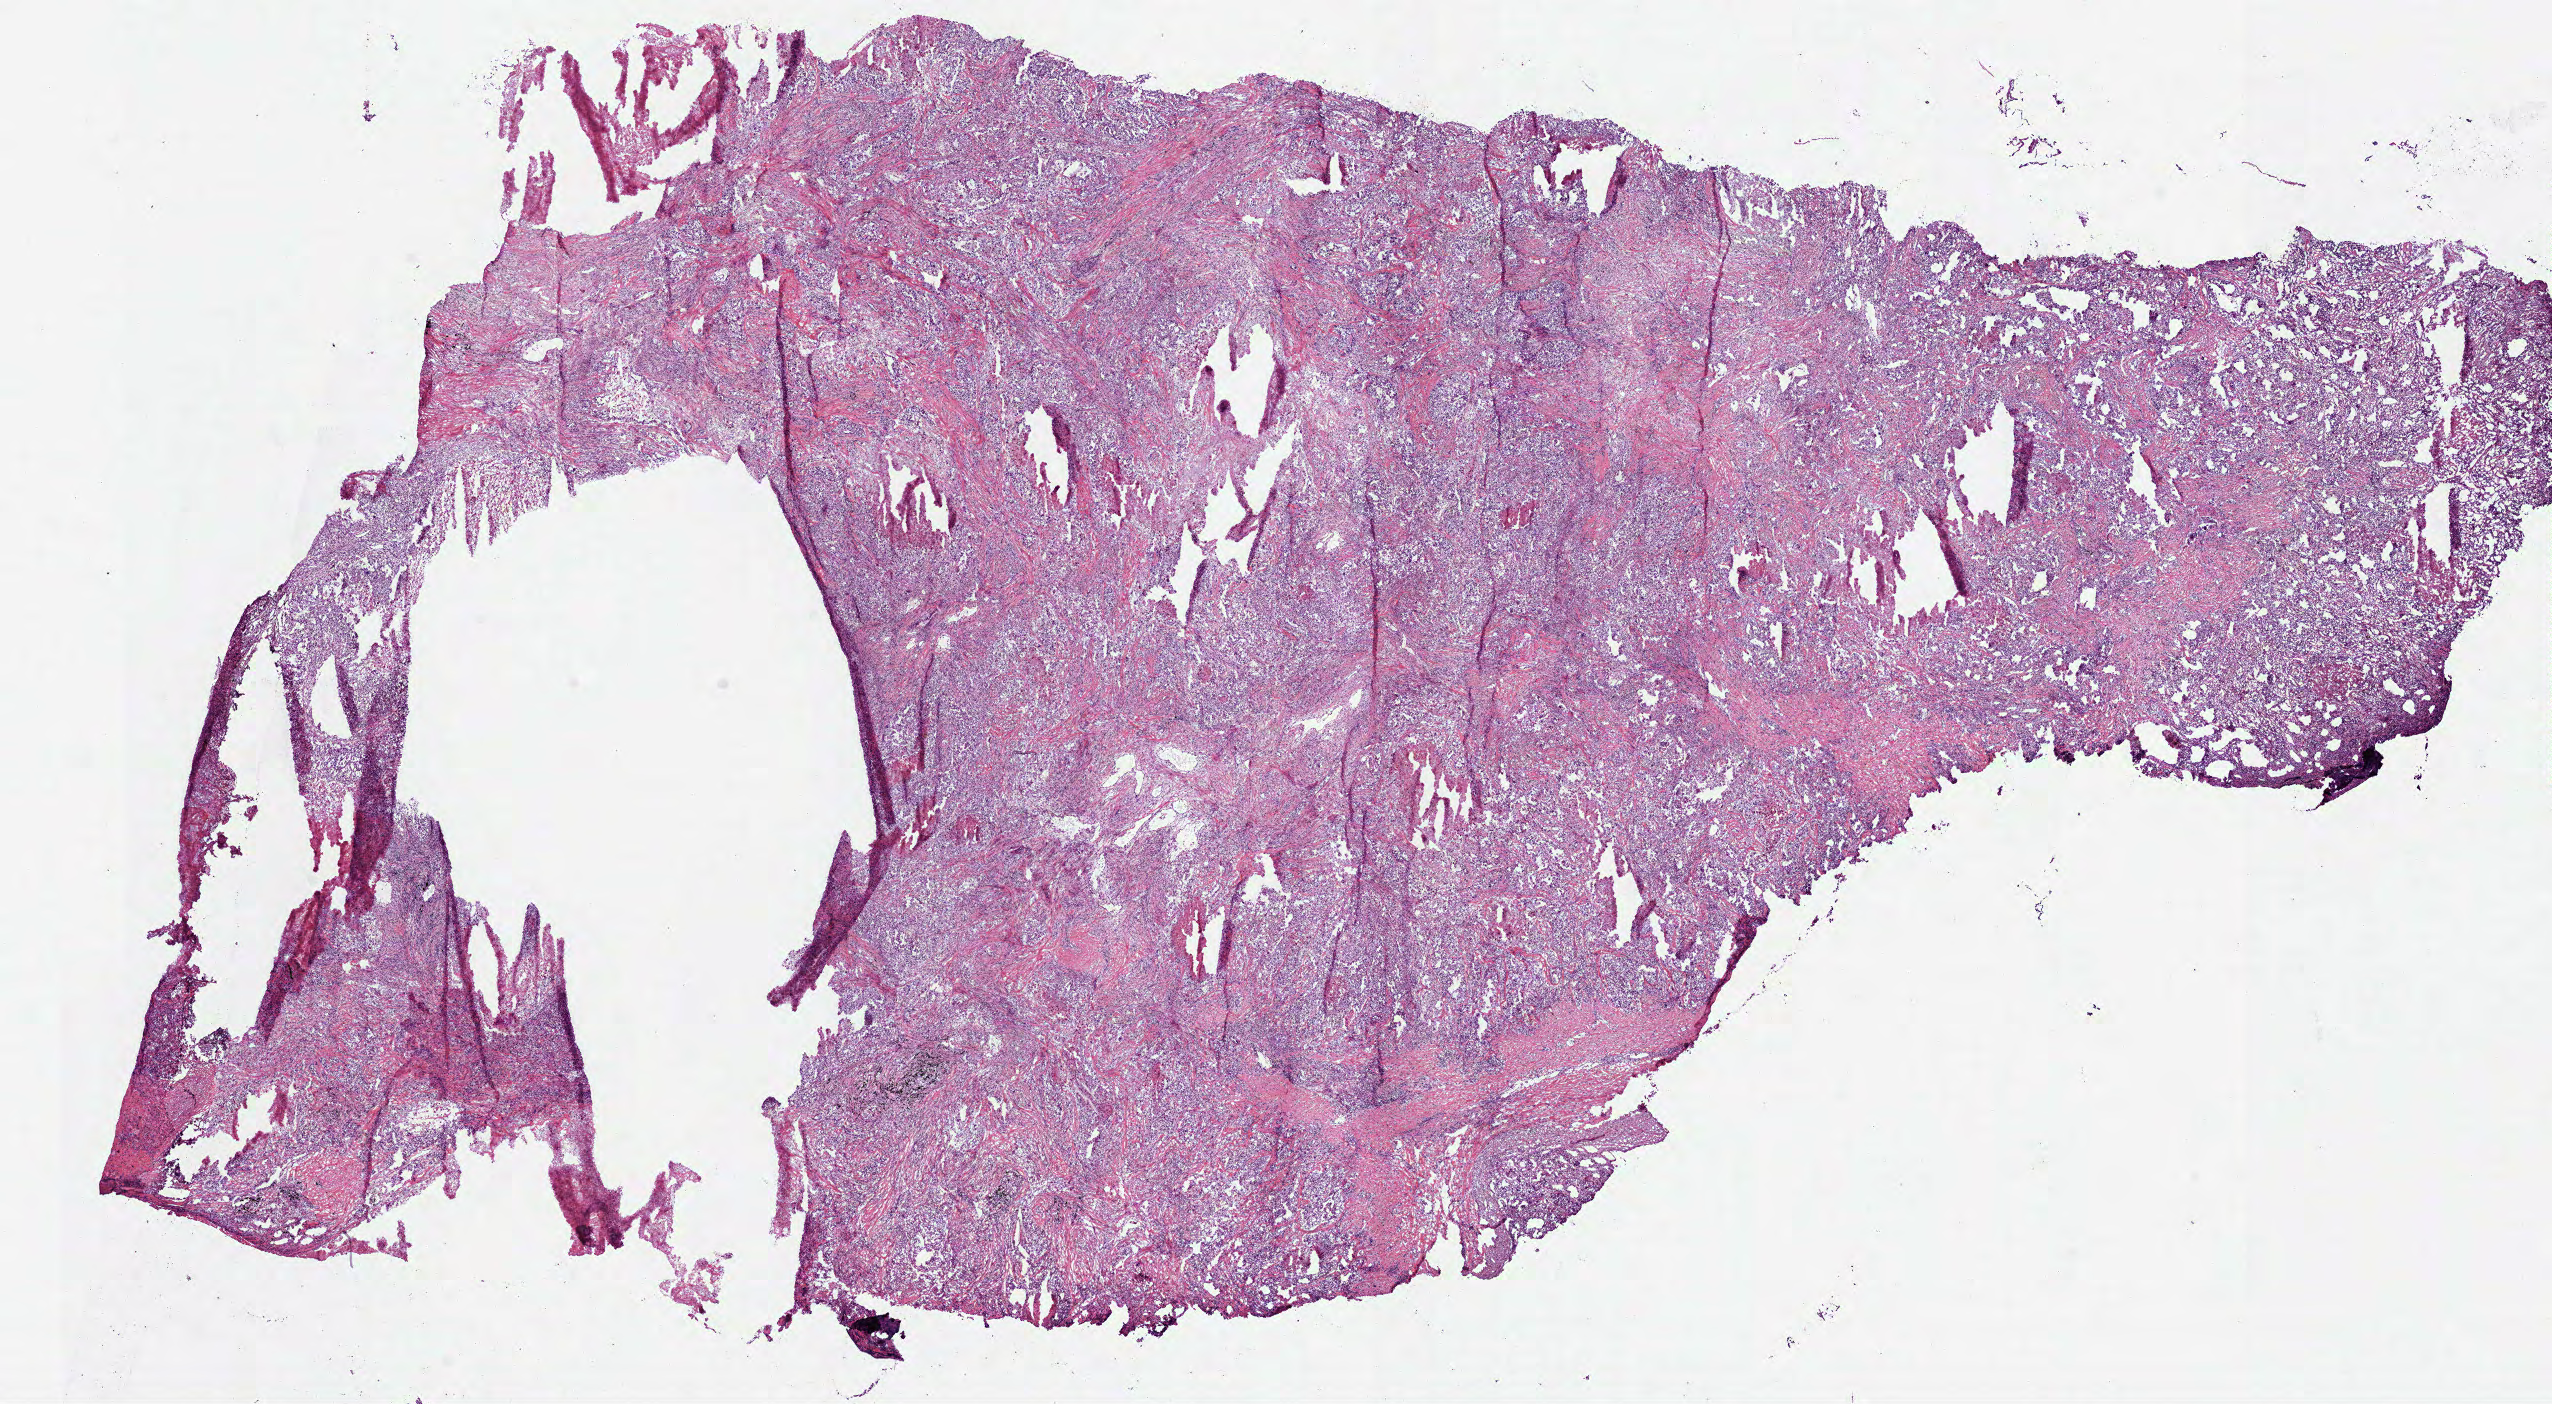
Whole-slide histology image, H&E-stained — whole scanned area (about 20.6 x 11.3 mm) shown as a low-resolution overview, frozen section from the bottom of the tissue portion, lung, primary tumour sample. Male patient; age at initial diagnosis 72 years. Pathologist review of this section (percent, as recorded): tumour cells 90%, tumour nuclei 70%, normal cells 0%, stromal cells 0%, necrosis 10%. Inflammatory infiltration, as recorded: lymphocyte infiltration 10%, monocyte infiltration 2%, neutrophil infiltration 5%.
TNM: T4 N2 M0. AJCC pathologic stage: IIIB (5th edition). Diagnosis: Adenocarcinoma, NOS (lower lobe, lung). Laterality: left.